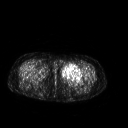
FDG PET of an extremity soft-tissue mass (from a PET/CT study), one axial slice. Slice 246 of 267 in the series (ordered by position). 3.27 mm slice thickness. 128 × 128 image matrix, field of view 500 × 500 mm. Patient: female, 42 years. Case-level facts recorded for this patient, not image findings: histological type: pleiomorphic leiomyosarcoma; grade: intermediate; site of the primary tumour: left thigh.
Annotated regions visible in this slice (expert contour drawn on MRI and transferred to this co-registered scan by the dataset authors):
- gross tumour volume including surrounding oedema: bounding box [x1, y1, x2, y2] px = [60, 64, 82, 82]
- gross tumour volume (mass): [60, 64, 82, 81]